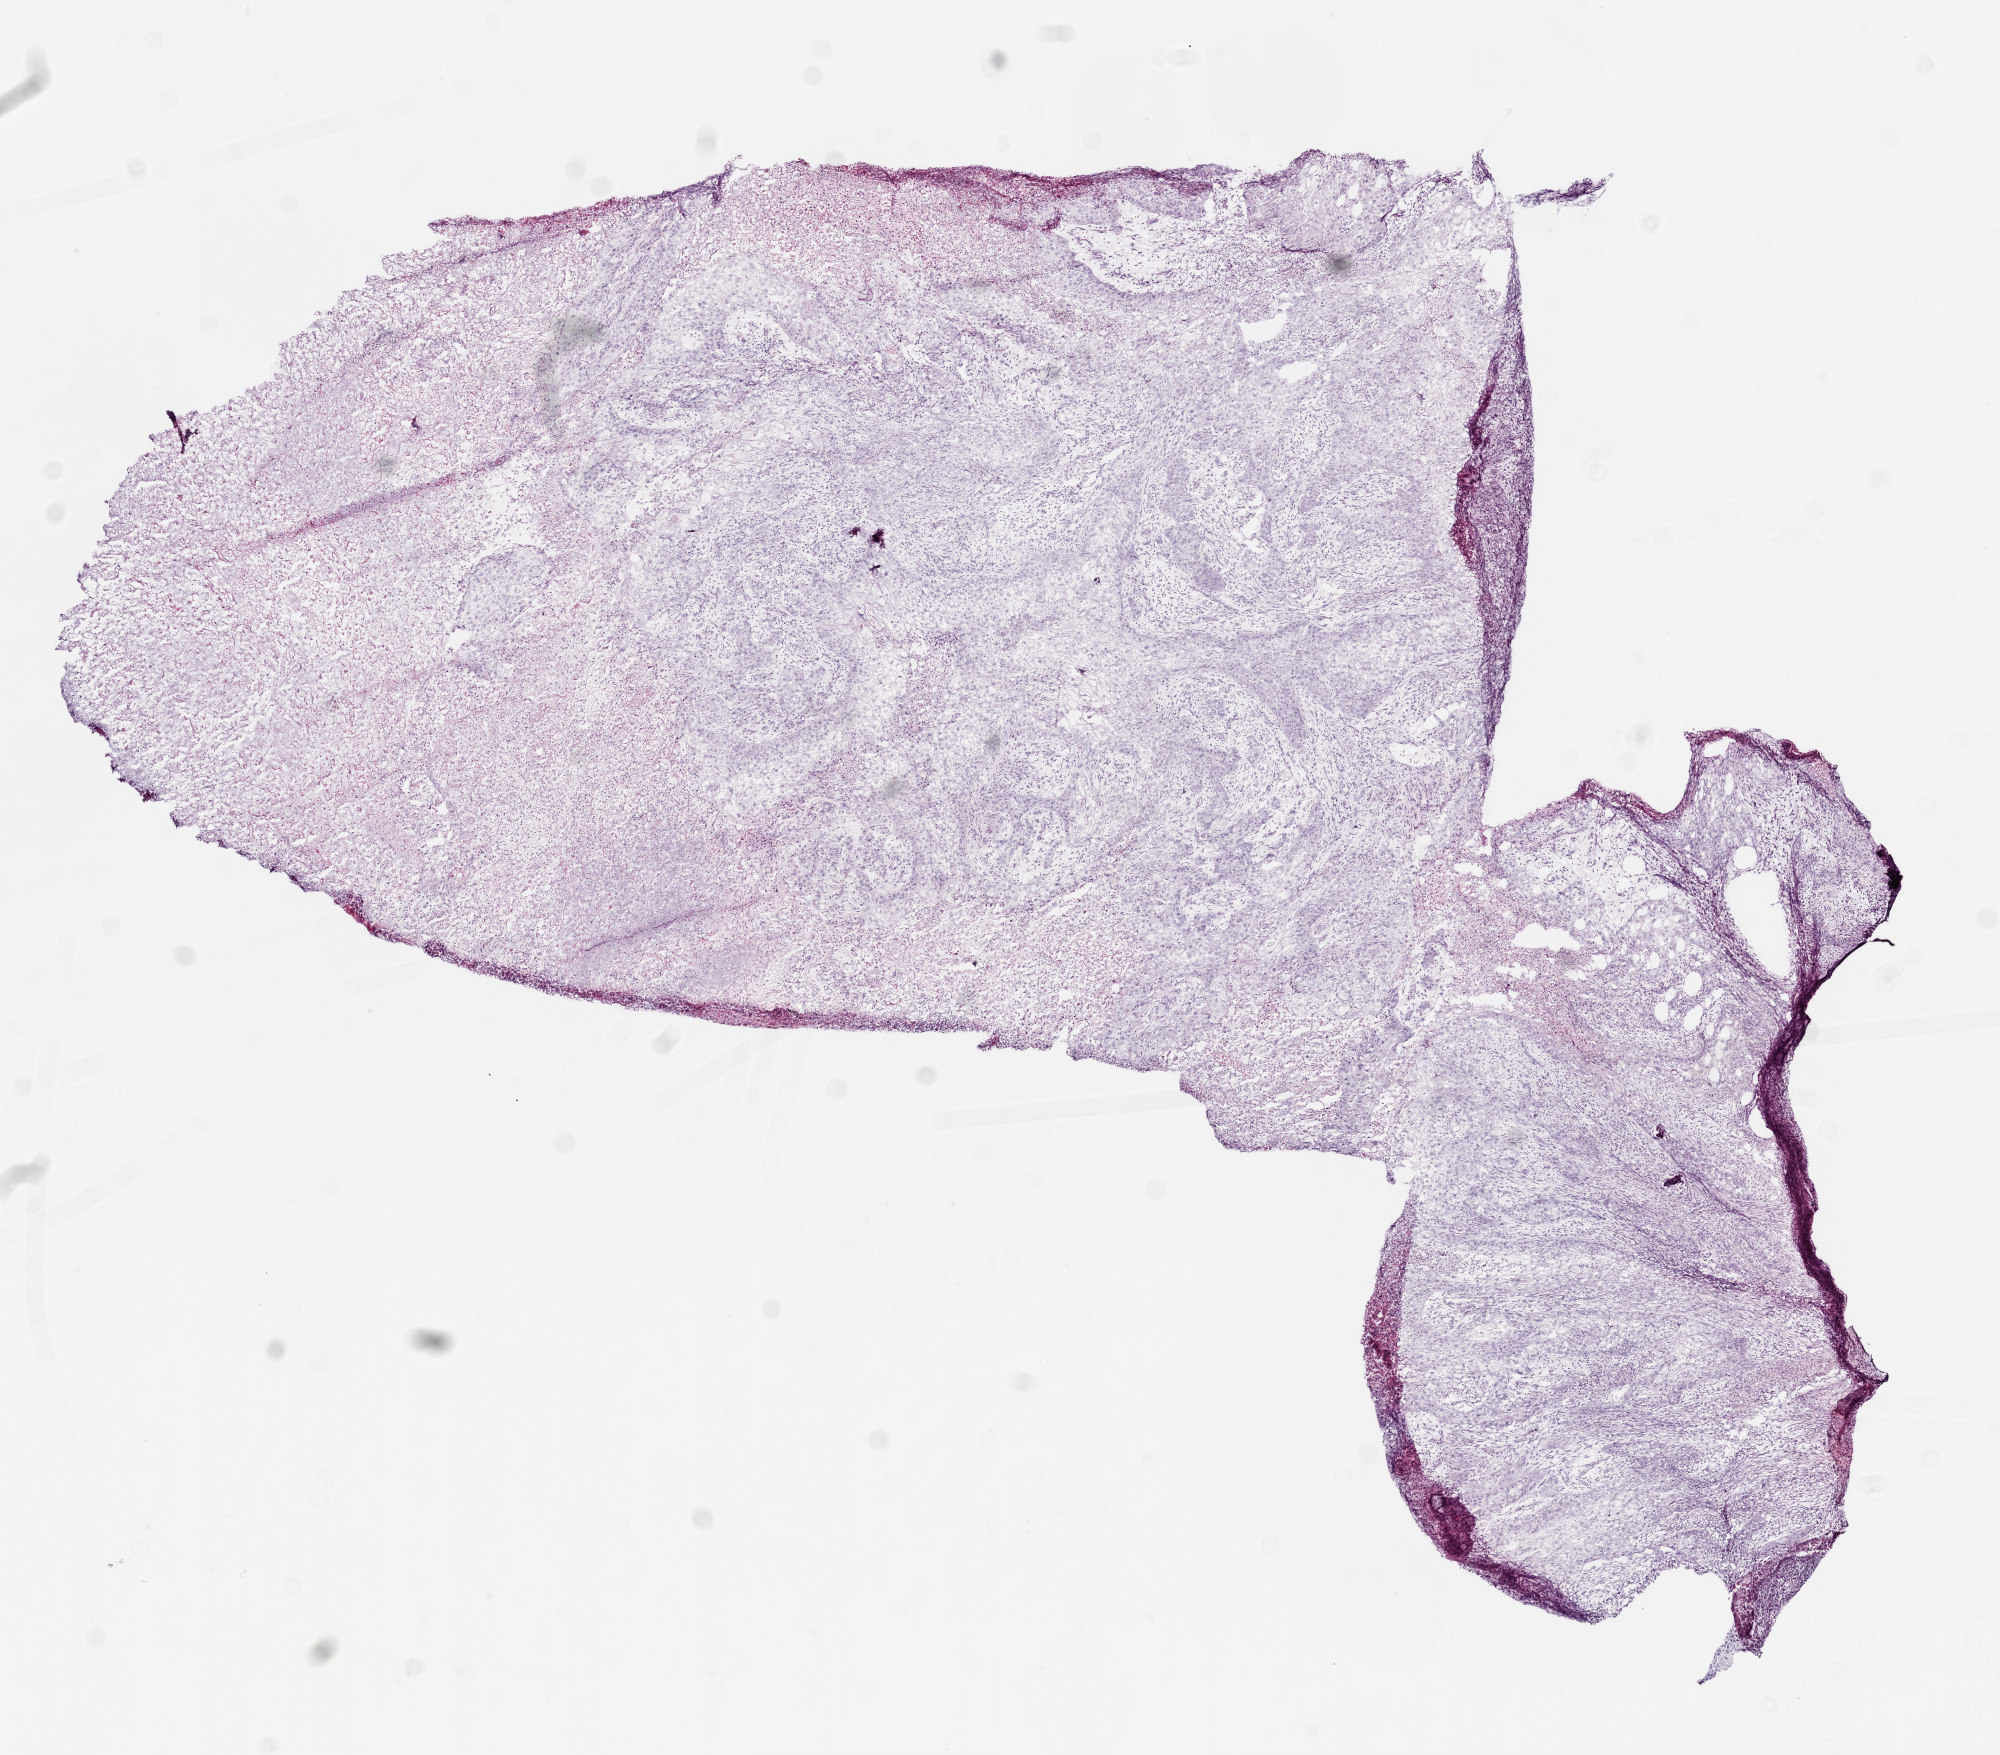
Digitized H&E-stained tissue section (whole slide), shown as a low-resolution overview of the whole scanned area (about 8.0 x 7.0 mm, acquisition: 20x scan), frozen section from the top of the tissue portion, primary tumour sample from the lung. Patient: male, age at initial diagnosis 47 years. Pathologist review of this section (percent, as recorded): tumour cells 75%, tumour nuclei 85%.
Pathologic diagnosis: Squamous cell carcinoma, NOS.